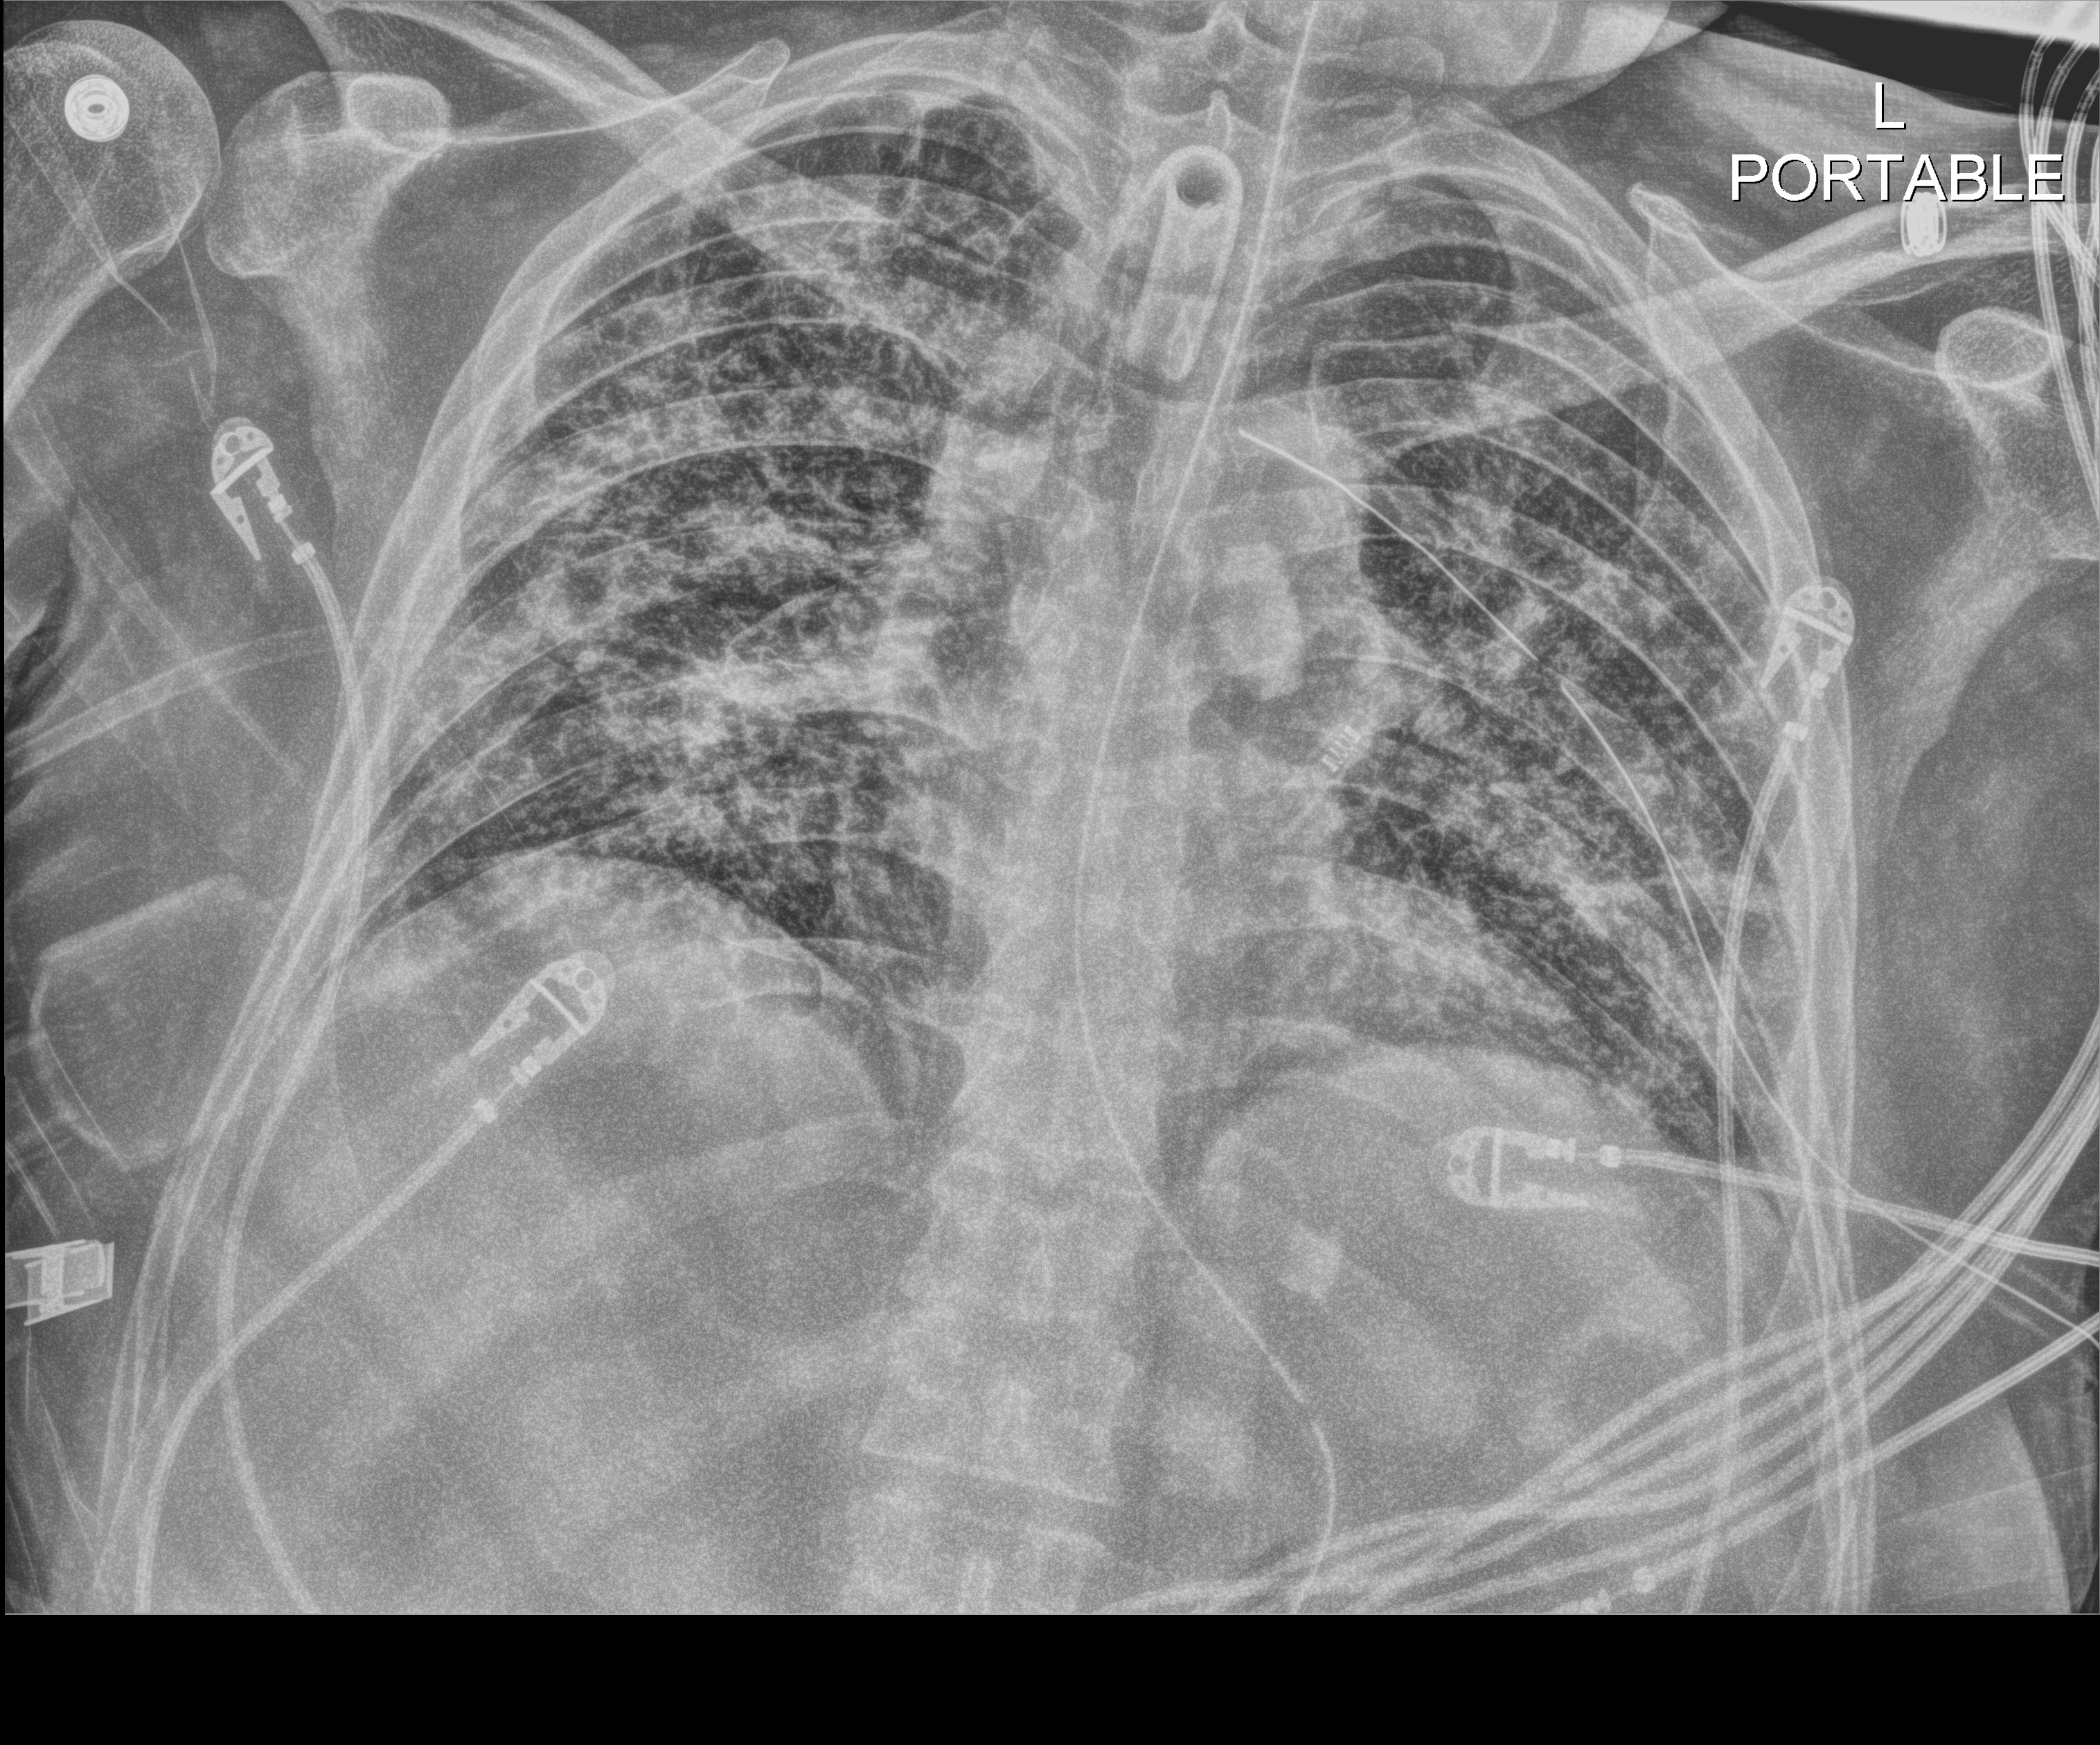
Bedside chest radiograph (digital radiography), anteroposterior (AP) projection. Patient hospitalised with COVID-19; male, aged 18–59 years.
Admission-level facts for this patient (not findings on this image; timing relative to this image not recorded):
- length of hospital stay: 63 days
- mechanically ventilated during this hospital stay: yes